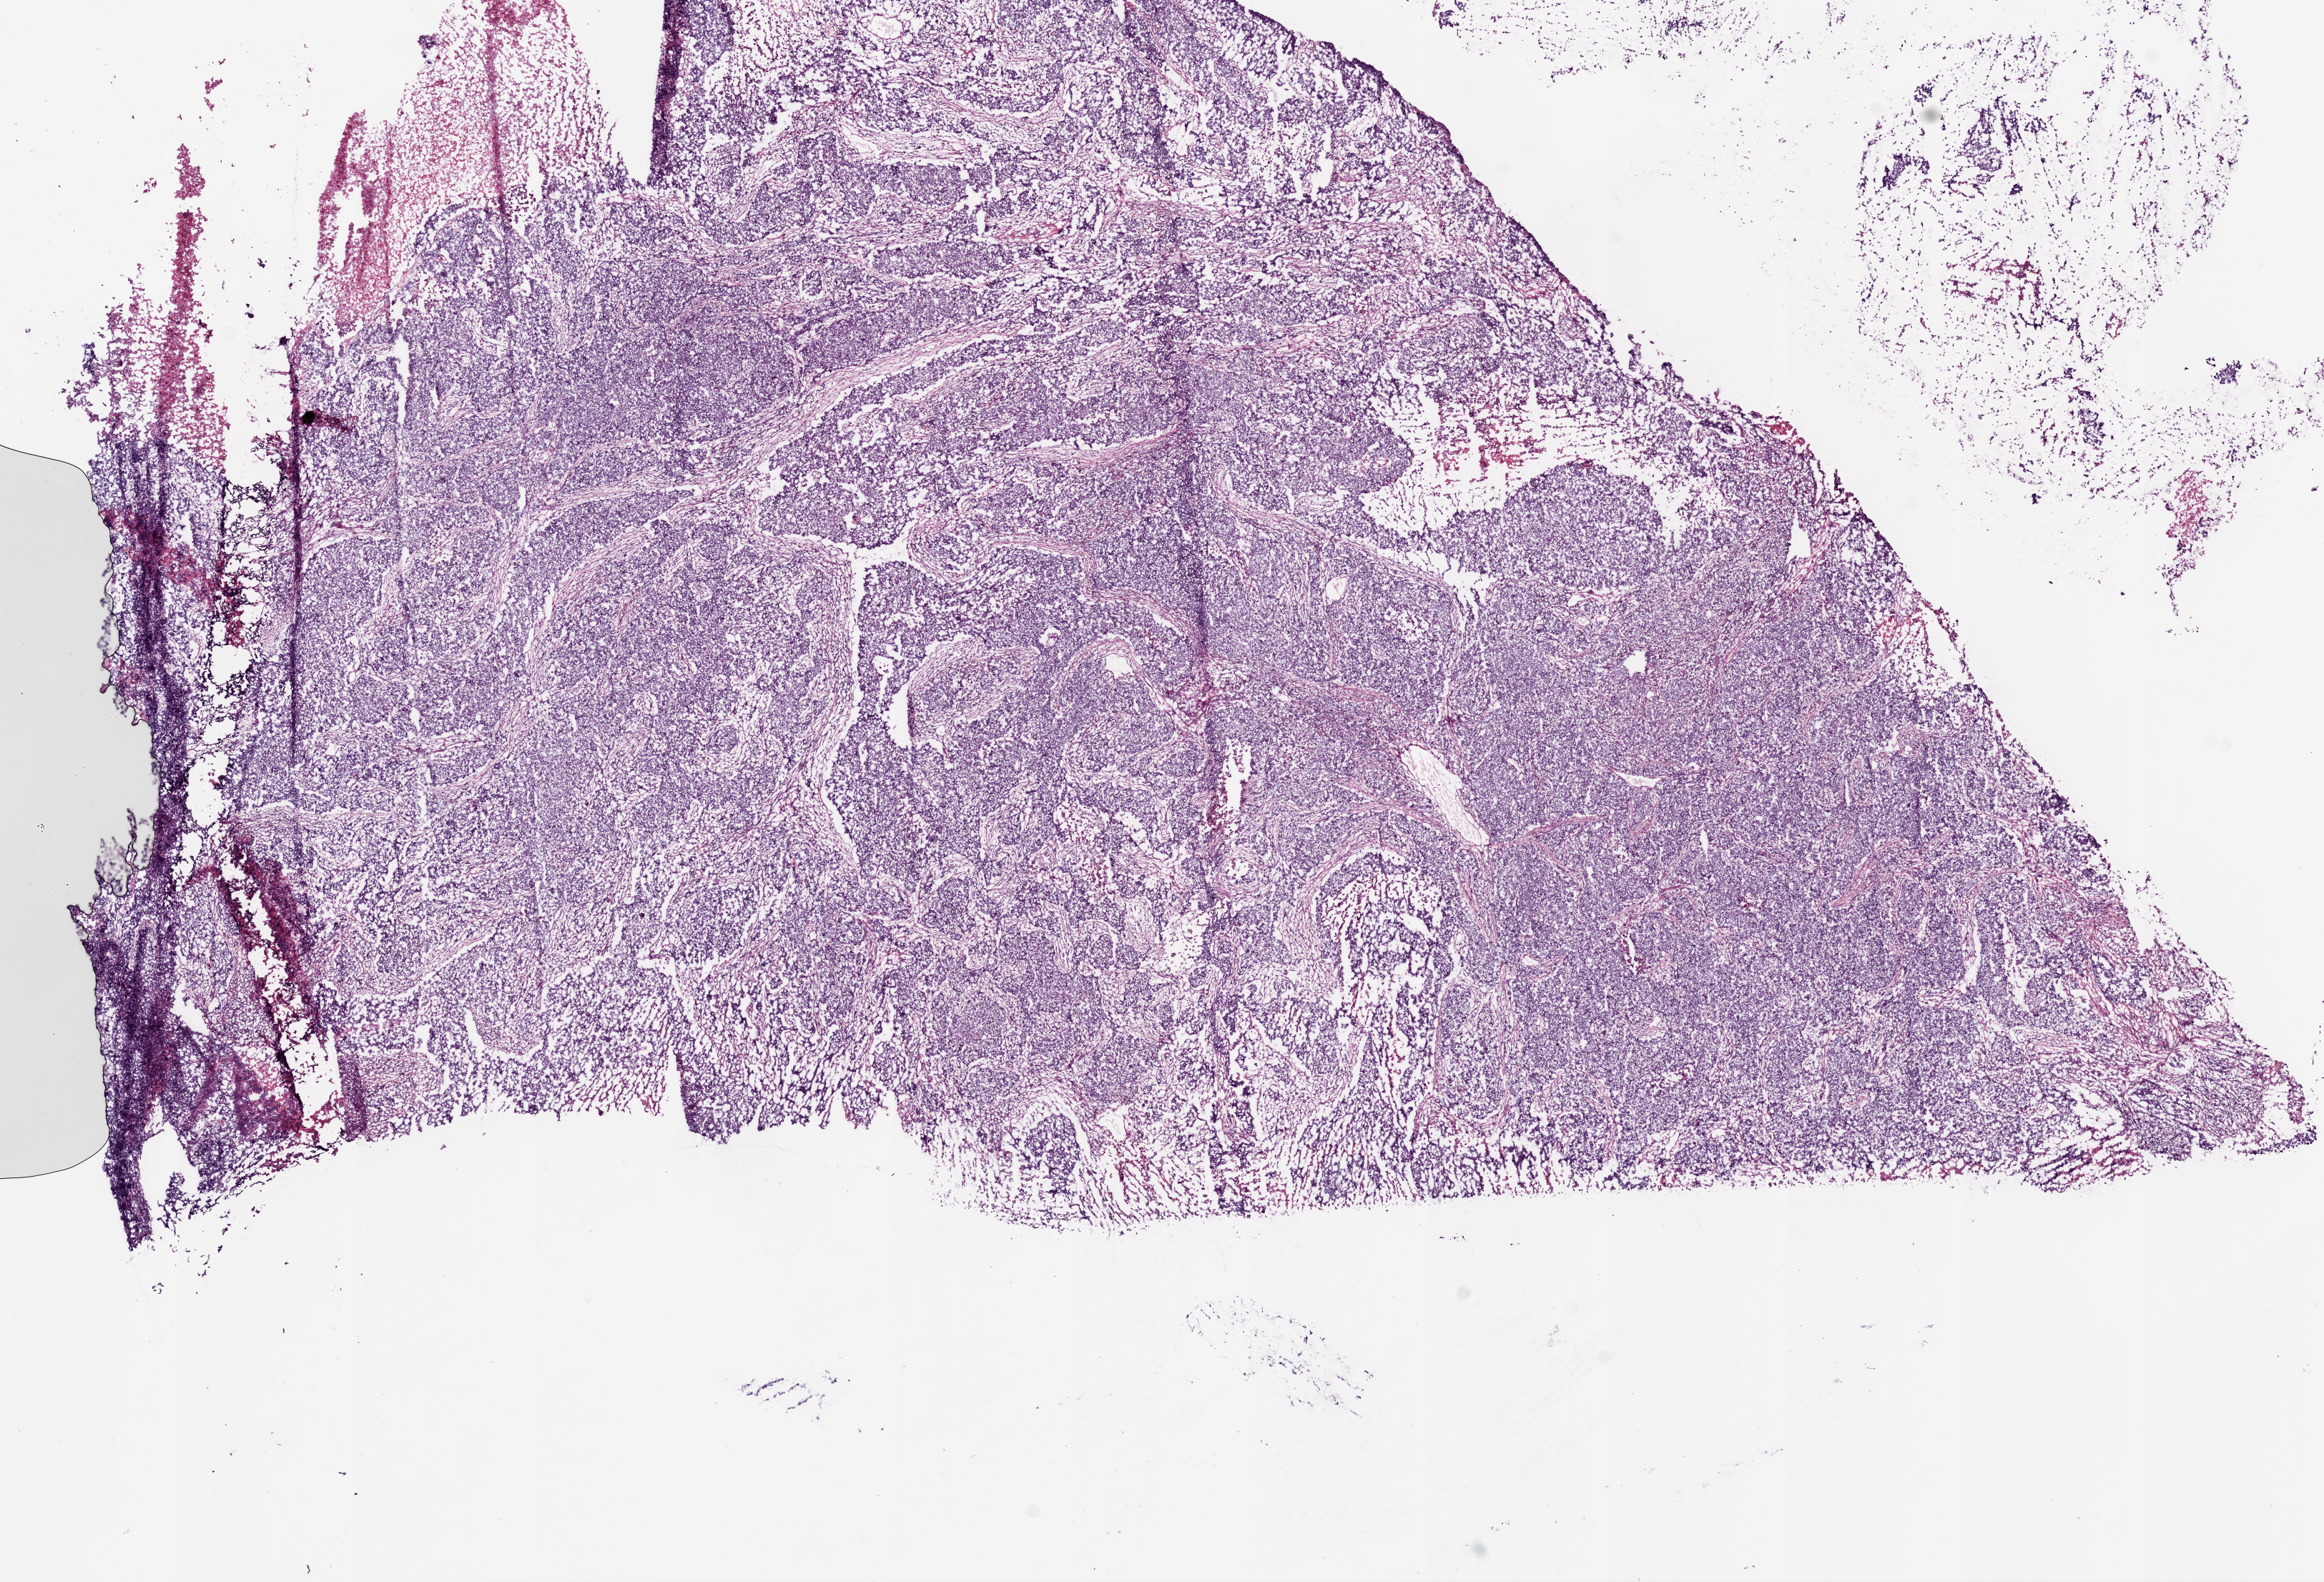
Digitized Hematoxylin and eosin (H&E) stained tissue section (whole slide), whole scanned area (about 13.0 x 8.9 mm) shown as a low-resolution overview. Frozen section from the bottom of the tissue portion. Primary tumour sample from the lung. Female, age 75 years at initial diagnosis. Pathologist review of this section (percent, as recorded): tumour cells 80%, tumour nuclei 80%, normal cells 0%, stromal cells 10%, necrosis 10%.
Histologic diagnosis: Papillary adenocarcinoma, NOS (upper lobe, lung). Laterality: right. AJCC pathologic stage: IB.